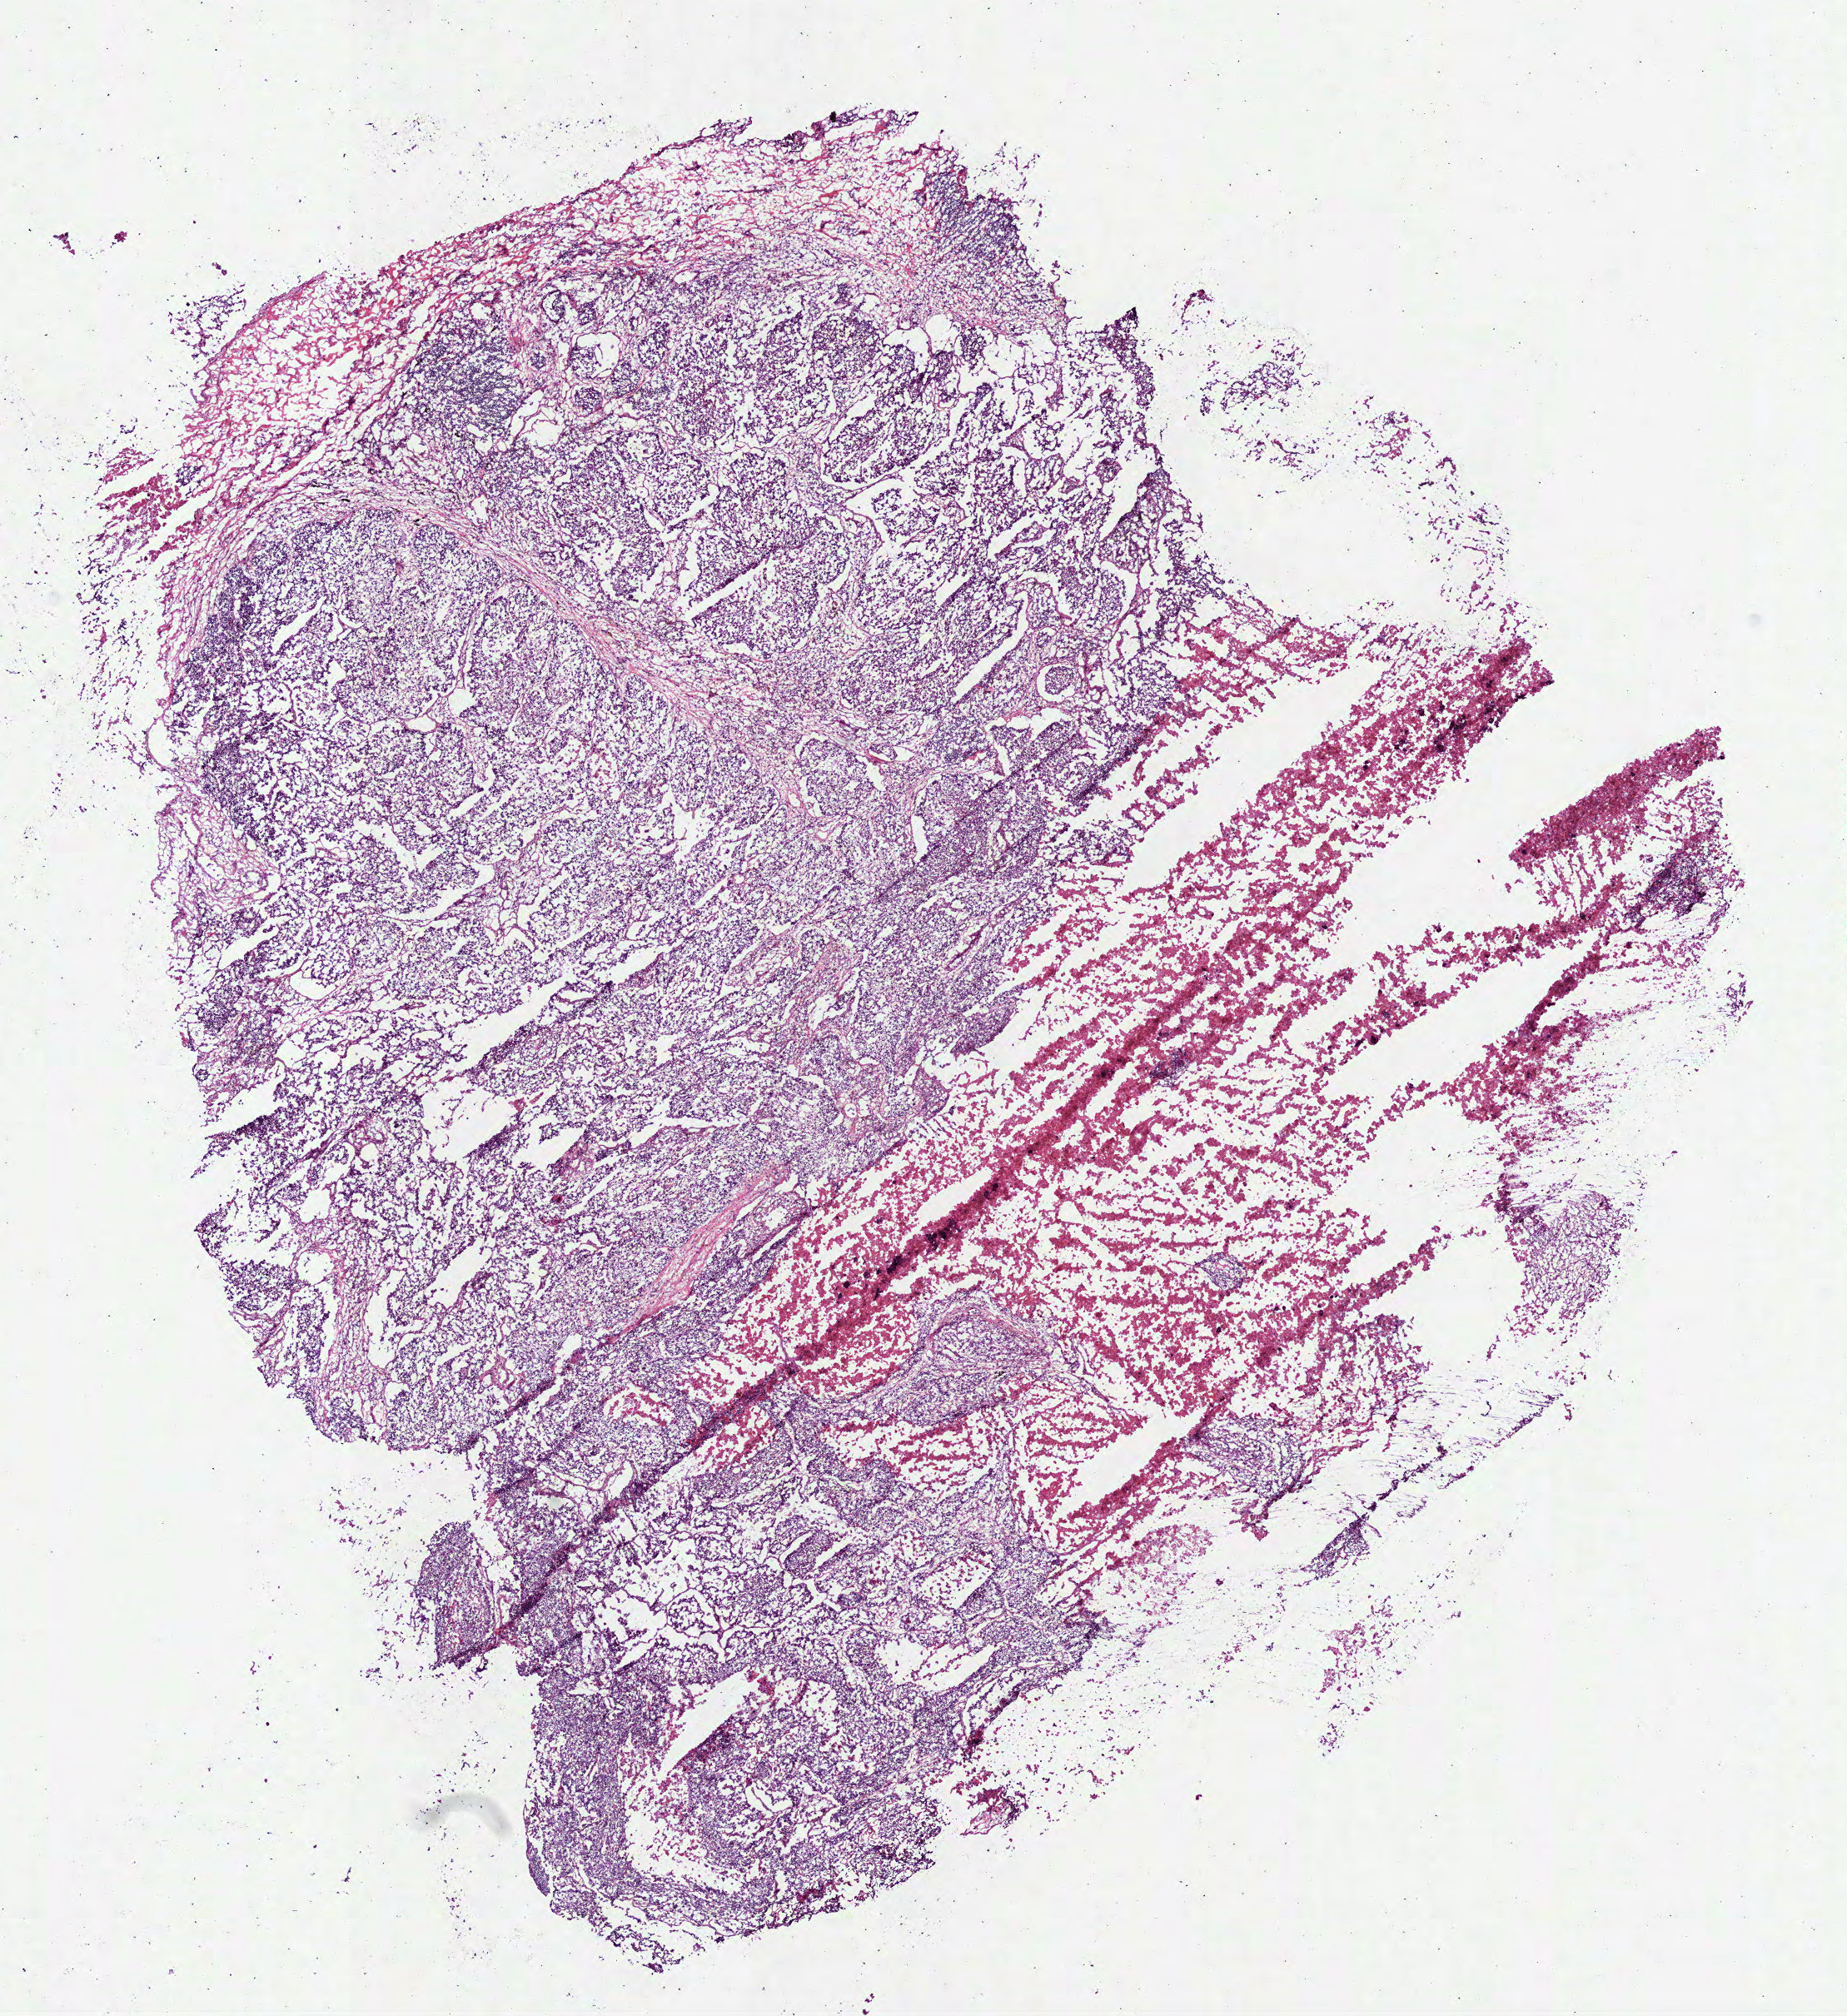
H&E whole-slide image — low-resolution overview of the scanned area, about 8.9 x 9.8 mm; frozen section; sample: primary tumour, lung. Patient: female, age at initial diagnosis 71 years. Composition of this section per pathologist review: tumour cells 70%, tumour nuclei 78%, normal cells 5%, stromal cells 10%, necrosis 15%. Inflammatory infiltration, as recorded: lymphocyte infiltration 5%.
Laterality: right. AJCC pathologic stage: IIA (7th edition). Pathologic diagnosis: Squamous cell carcinoma, NOS (lower lobe, lung).